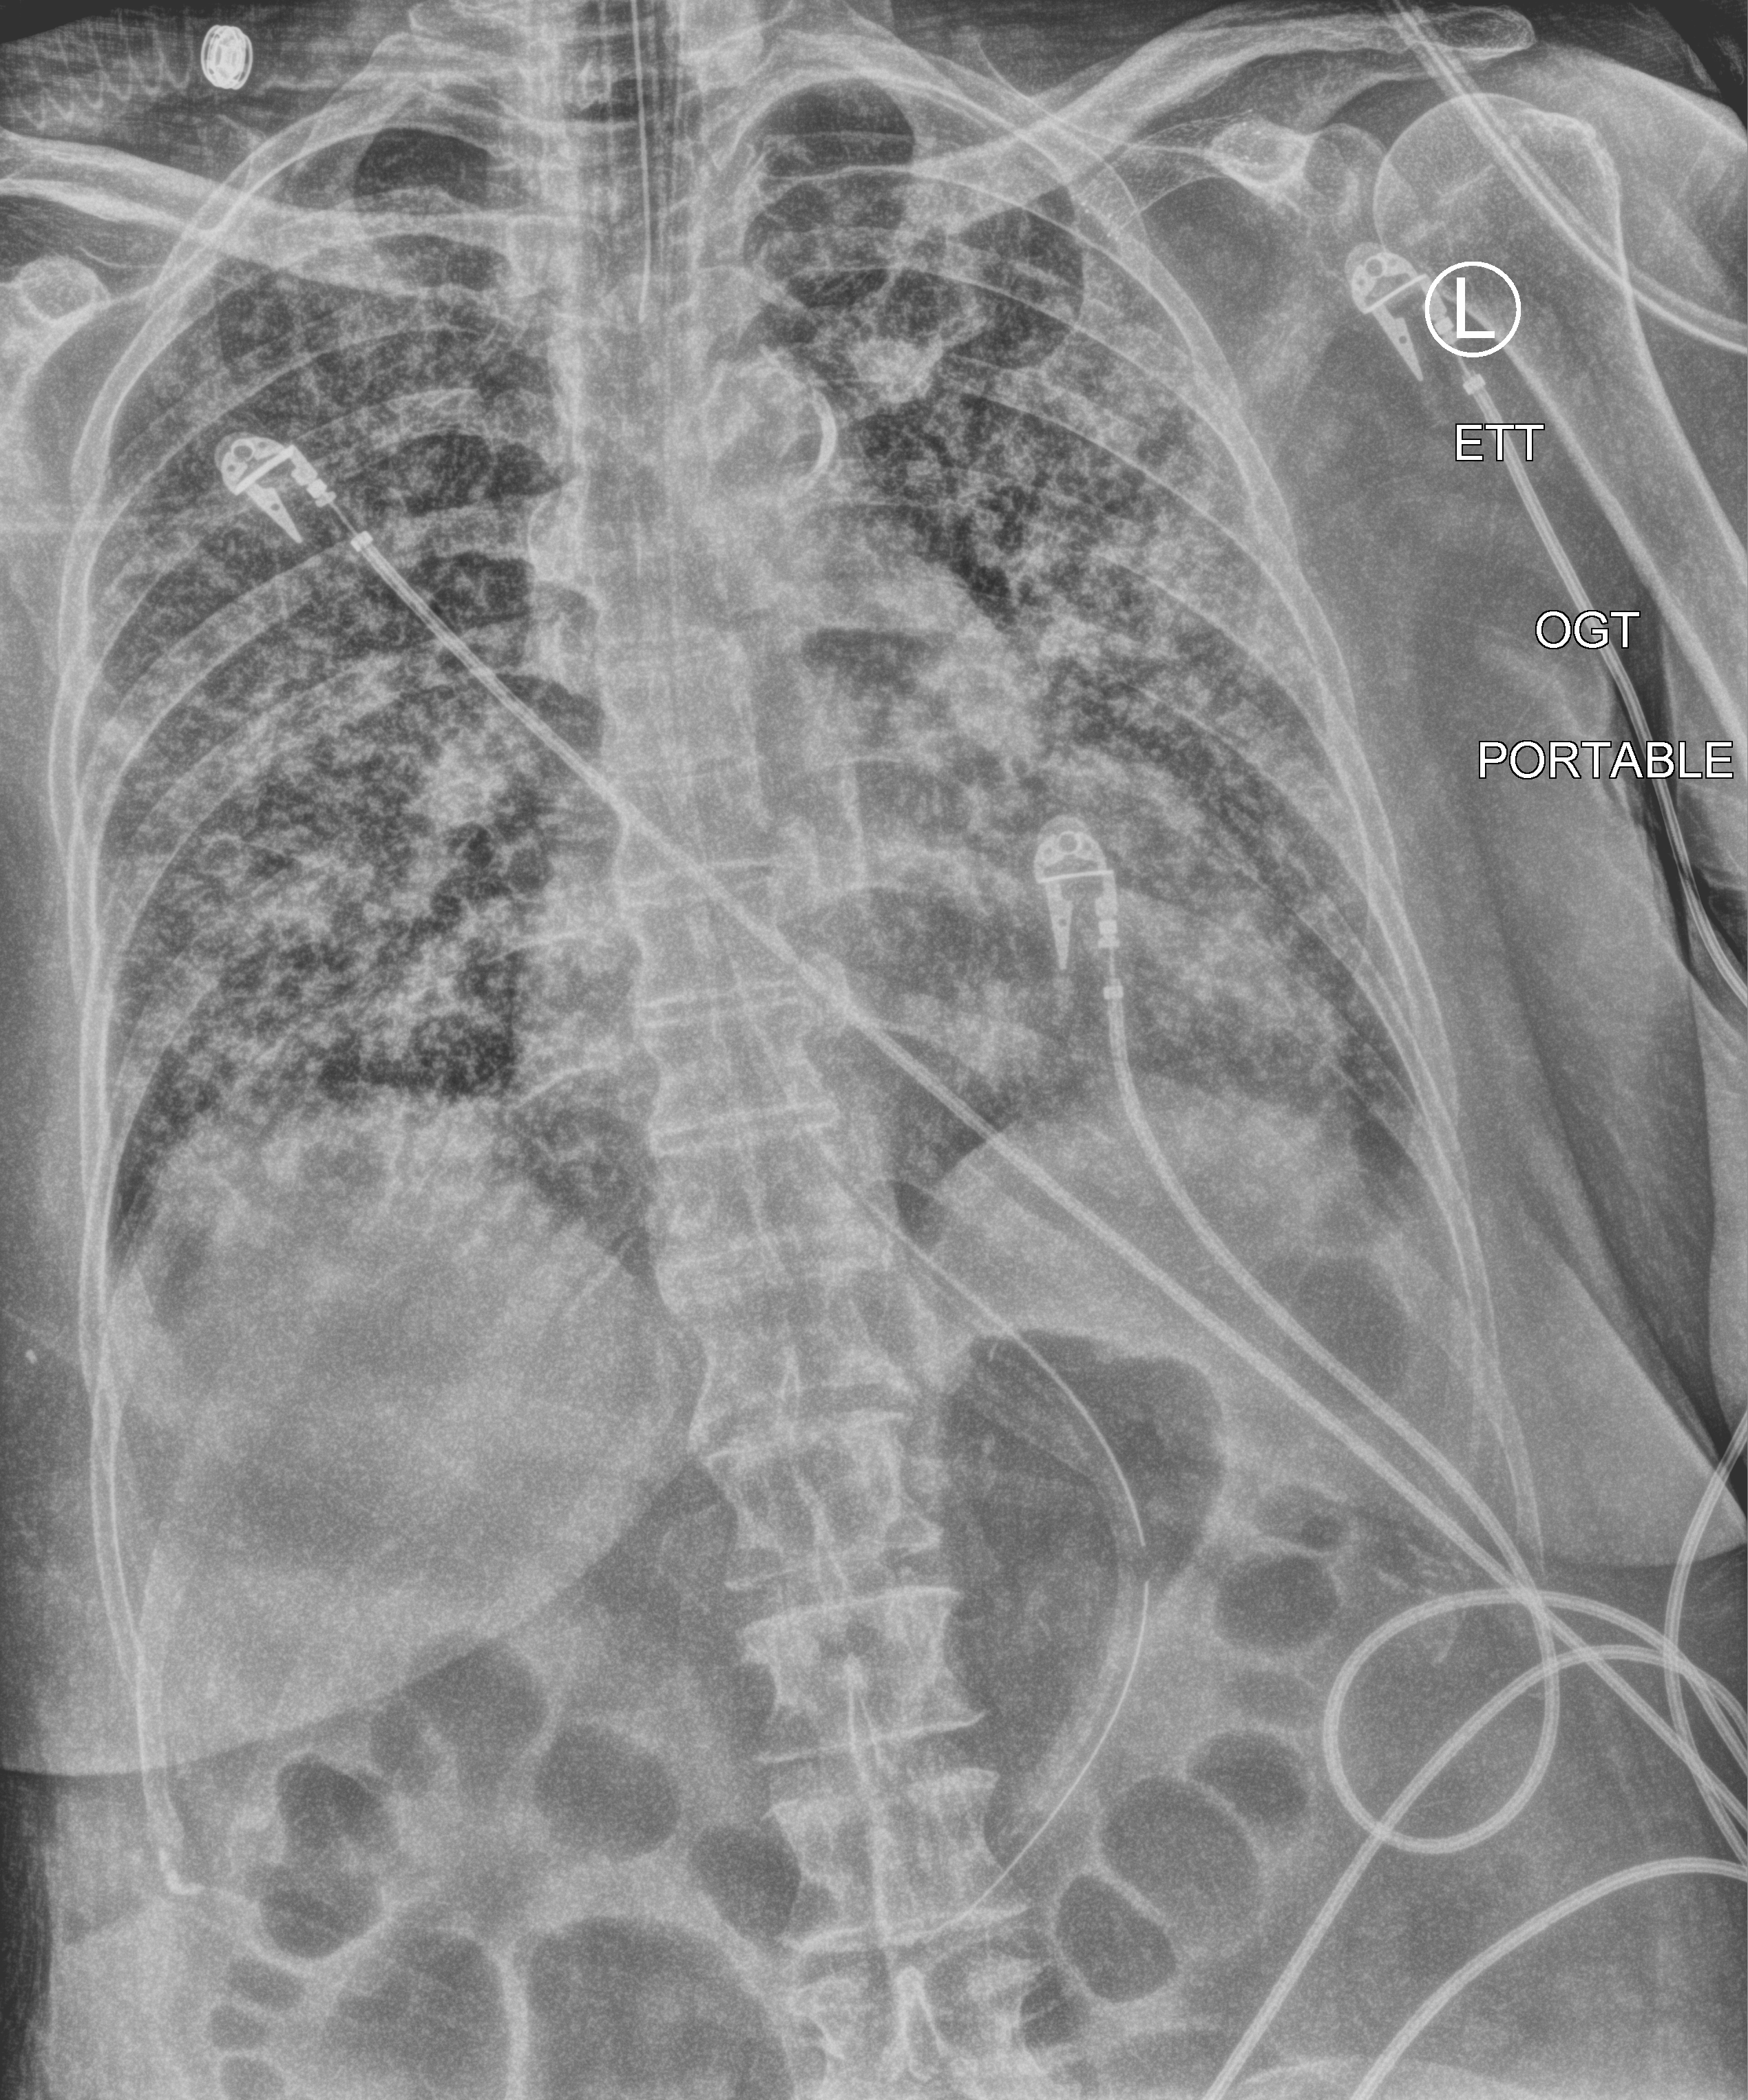
Bedside chest radiograph (computed radiography). Patient hospitalised with COVID-19; female, aged 60–74 years.
Hospital-stay facts (about this admission, not read from this image; timing relative to this image not recorded):
- chronic kidney disease (admission record): no
- mechanically ventilated during this hospital stay: yes